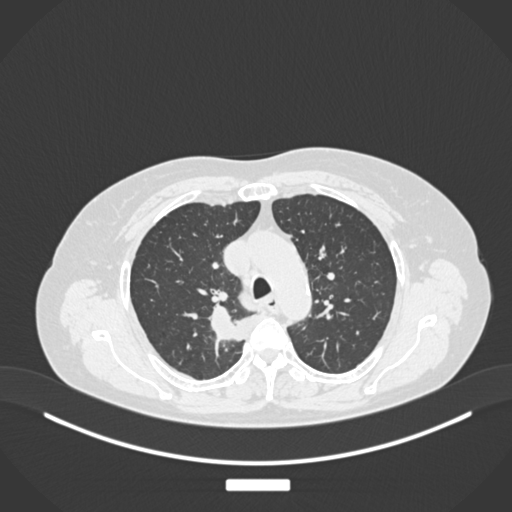
Chest CT, one axial slice. Position 187 of 237 along the scan axis. 120 kVp. Lung window (W 1500 / L -600 HU). 1 mm slice thickness. 512 × 512 image matrix. Female patient, age 62 years. Case-level facts recorded for this patient, not image findings: clinical TNM (as recorded): T1c N1 M0.
Outlined on this slice (rectangle marked by the reading radiologist):
- lung tumour (recorded histology: squamous cell carcinoma): bounding box (x1, y1, x2, y2) in pixels: (208, 302, 243, 344)